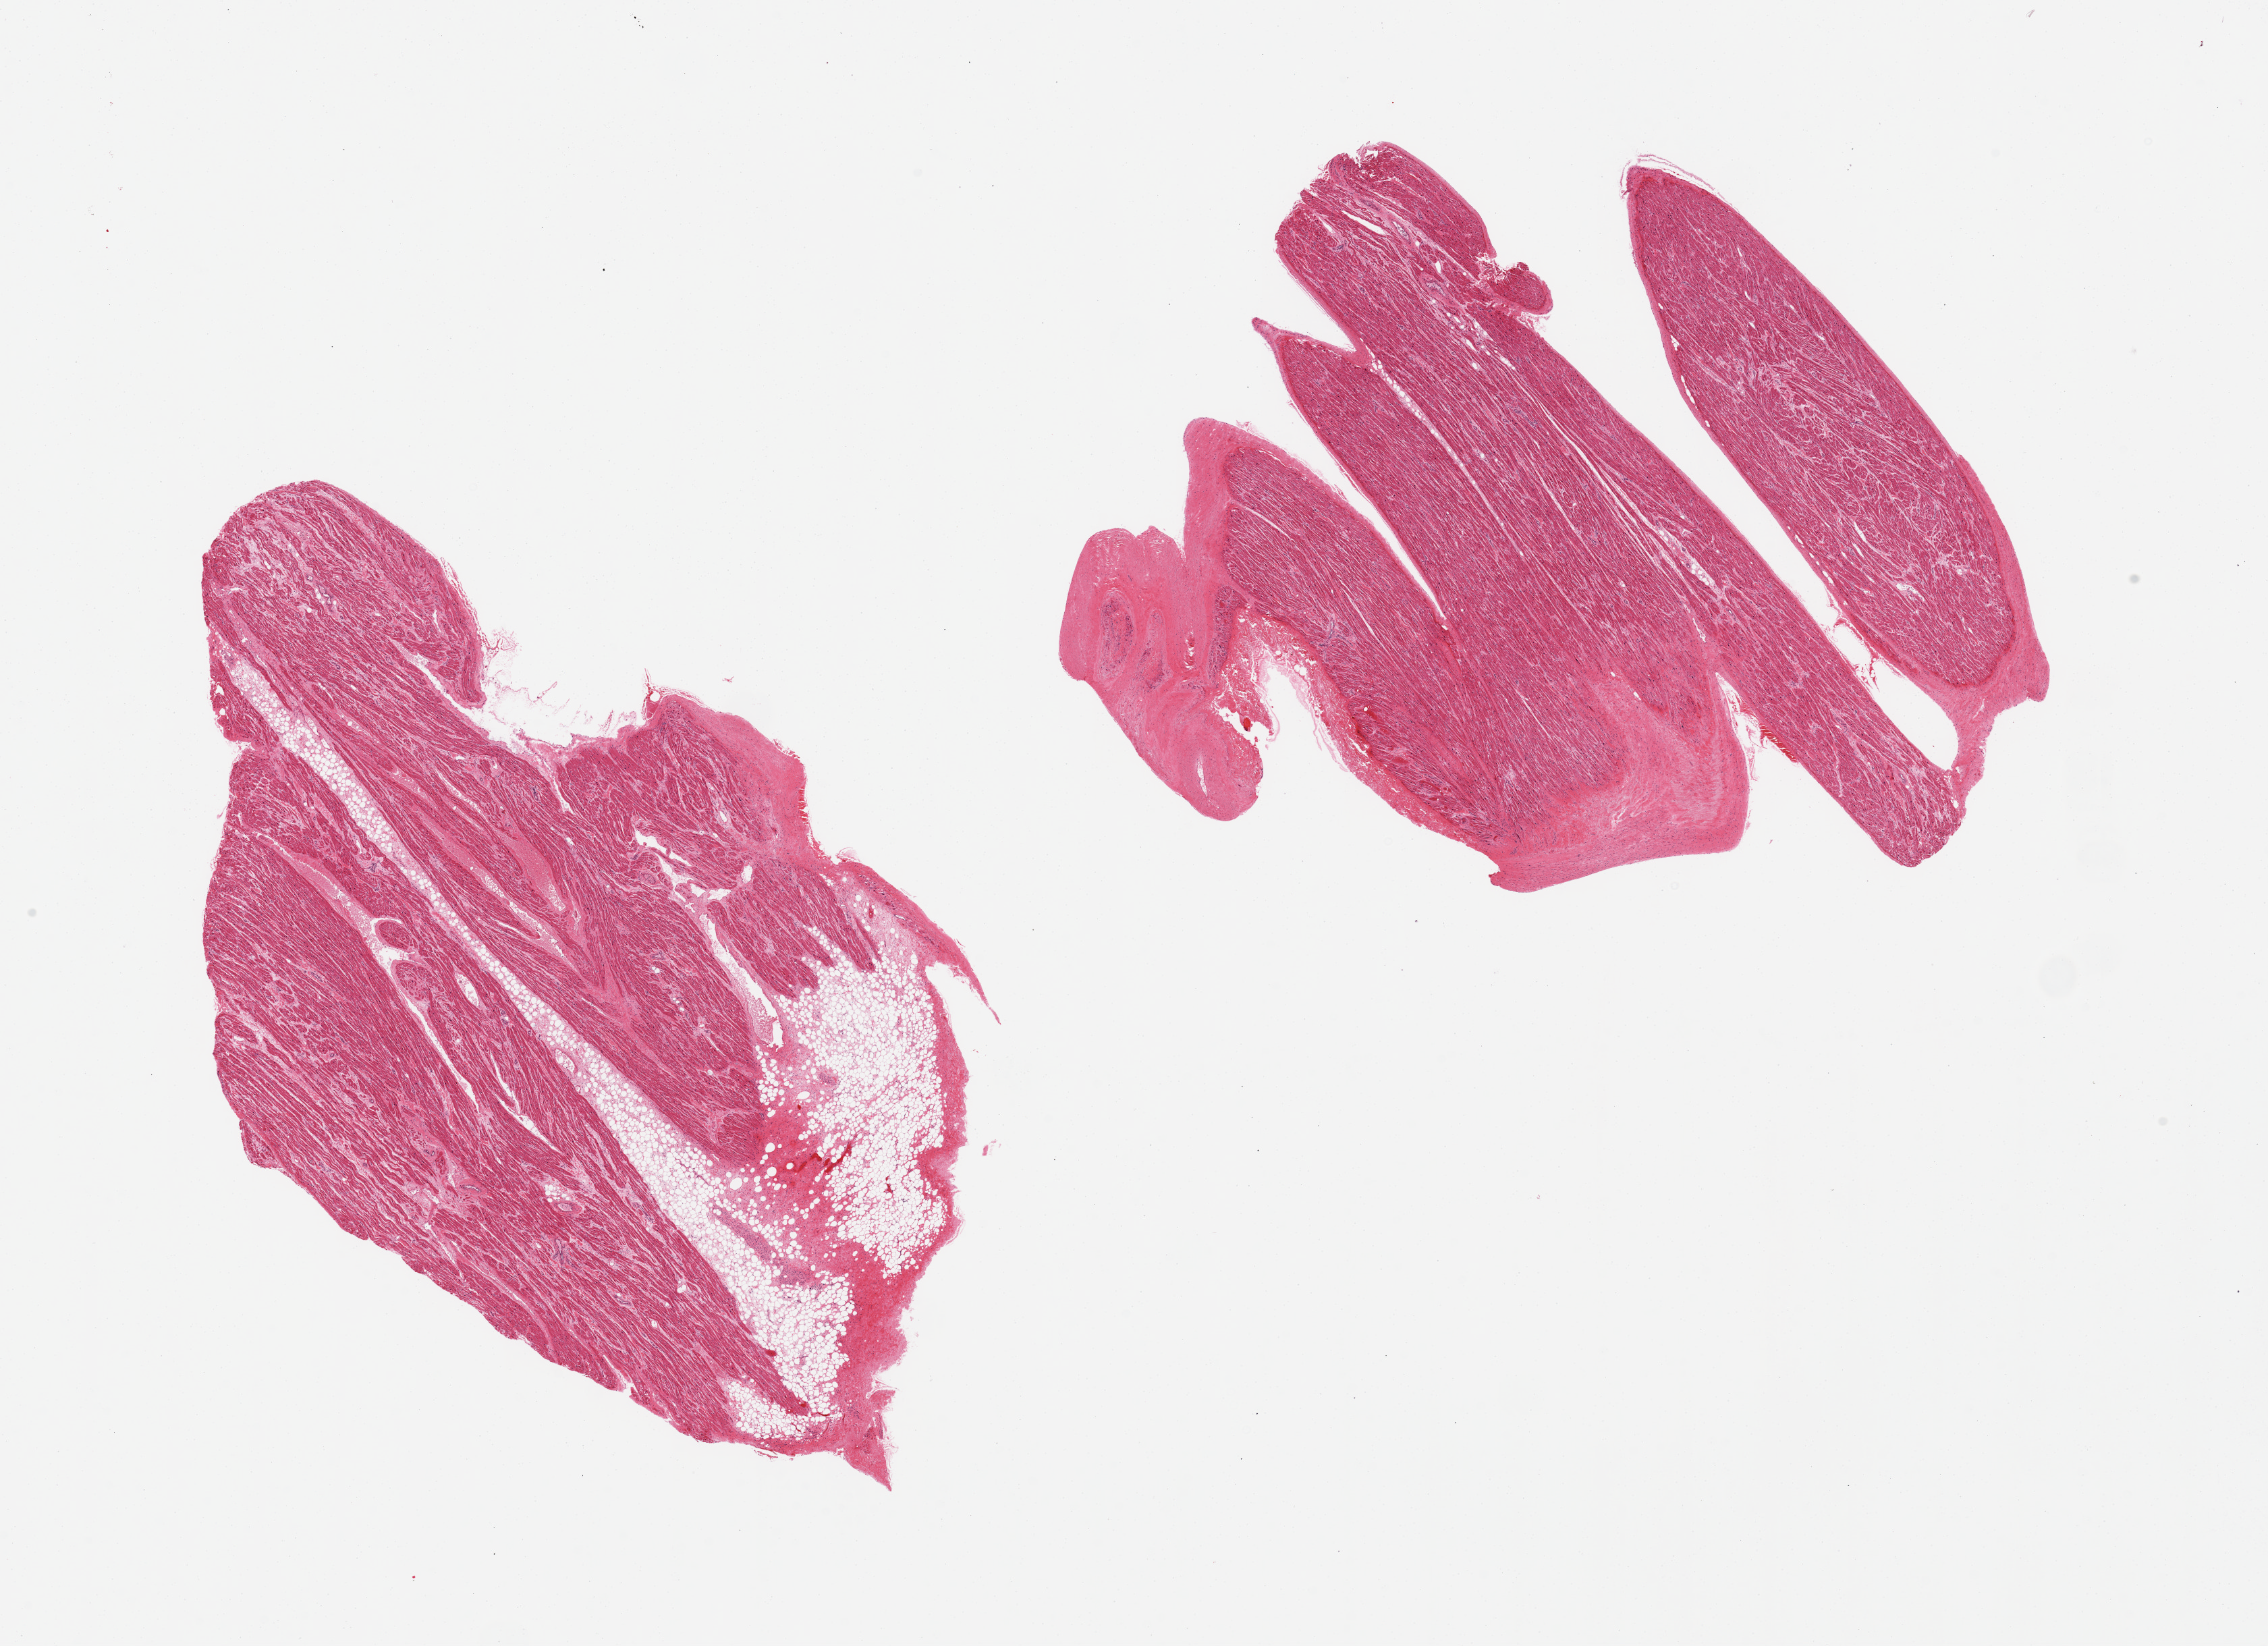
Digitized haematoxylin and eosin-stained section, brightfield — low-resolution overview of the scanned area, about 26.6 x 19.3 mm (acquisition: 20x scan); PAXgene-fixed paraffin-embedded (PFPE) section; sampled site (target tissue): auricular appendage; tissue donor sample. Donor: male.
Review note (as recorded): 2 pieces, one is ~25% fat, second includes 2 zones of fibrosis/old infarct.